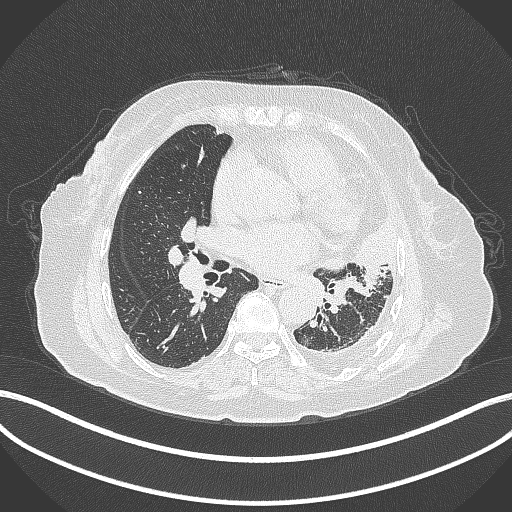
Chest CT, one axial slice; position 180 of 399 along the scan axis; reconstruction kernel B70f; 120 kVp; lung window (W 1500 / L -600 HU); 1 mm slice thickness; 512 × 512 image matrix. Female patient, age 75 years. Case-level facts recorded for this patient, not image findings: clinical TNM (as recorded): T3 N3 M1.
Outlined on this slice (rectangle marked by the reading radiologist):
- lung tumour (recorded histology: adenocarcinoma): box from (x=322, y=213) to (x=398, y=275) px